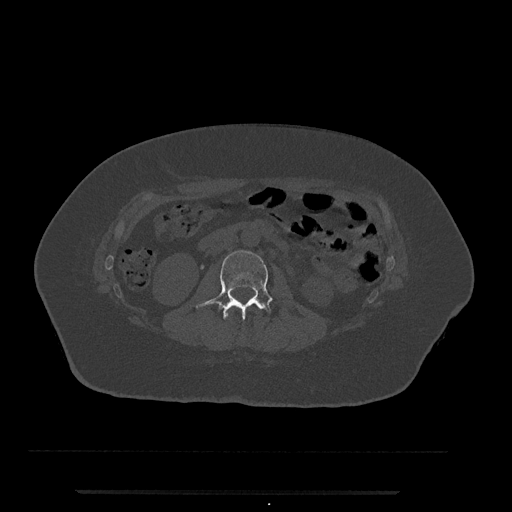
CT including the spine, one axial slice; slice 39 of 797 in the series (ordered by position); bone window (W 1800 / L 400 HU); 0.5 mm slice thickness; 512 × 512 image matrix, field of view 440 × 440 mm. Patient: female, 51 years. Case-level facts recorded for this patient, not image findings: primary cancer: neuro; vertebrae with lytic lesions (as recorded): T8.
Outlined on this slice (semi-automatically segmented with operator editing):
- L1 vertebra: box from (x=226, y=310) to (x=234, y=318) px
- L2 vertebra: (x=196, y=250)–(x=273, y=320)